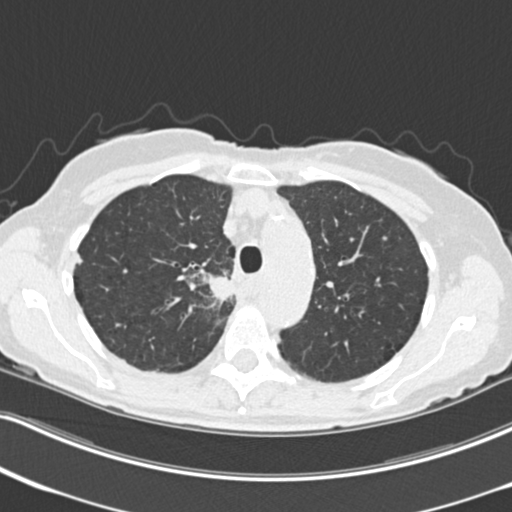
Low-dose screening chest CT, axial slice, third annual screen, lung window (W 1500 / L -600 HU), 2 mm slice thickness, standard (soft-tissue) reconstruction kernel (B30f), 120 kVp. Female, age 68 years at enrolment. Current smoker at enrolment.
Lesion marked by an expert reader, bounding box [x1, y1, x2, y2] px = [196, 268, 249, 324]. Screening reader's record for this exam (one nodule recorded; not confirmed to be the boxed lesion): non-calcified nodule or mass ≥4 mm, right upper lobe, 31 × 29 mm, poorly defined margins, soft tissue attenuation, pre-existing on the prior screen: no. Later outcome: lung cancer diagnosed 79 days after this screen — squamous cell carcinoma, NOS, right upper lobe, mediastinum, poorly differentiated (G3), stage IIIB (AJCC 6th edition), 43 mm at pathology.